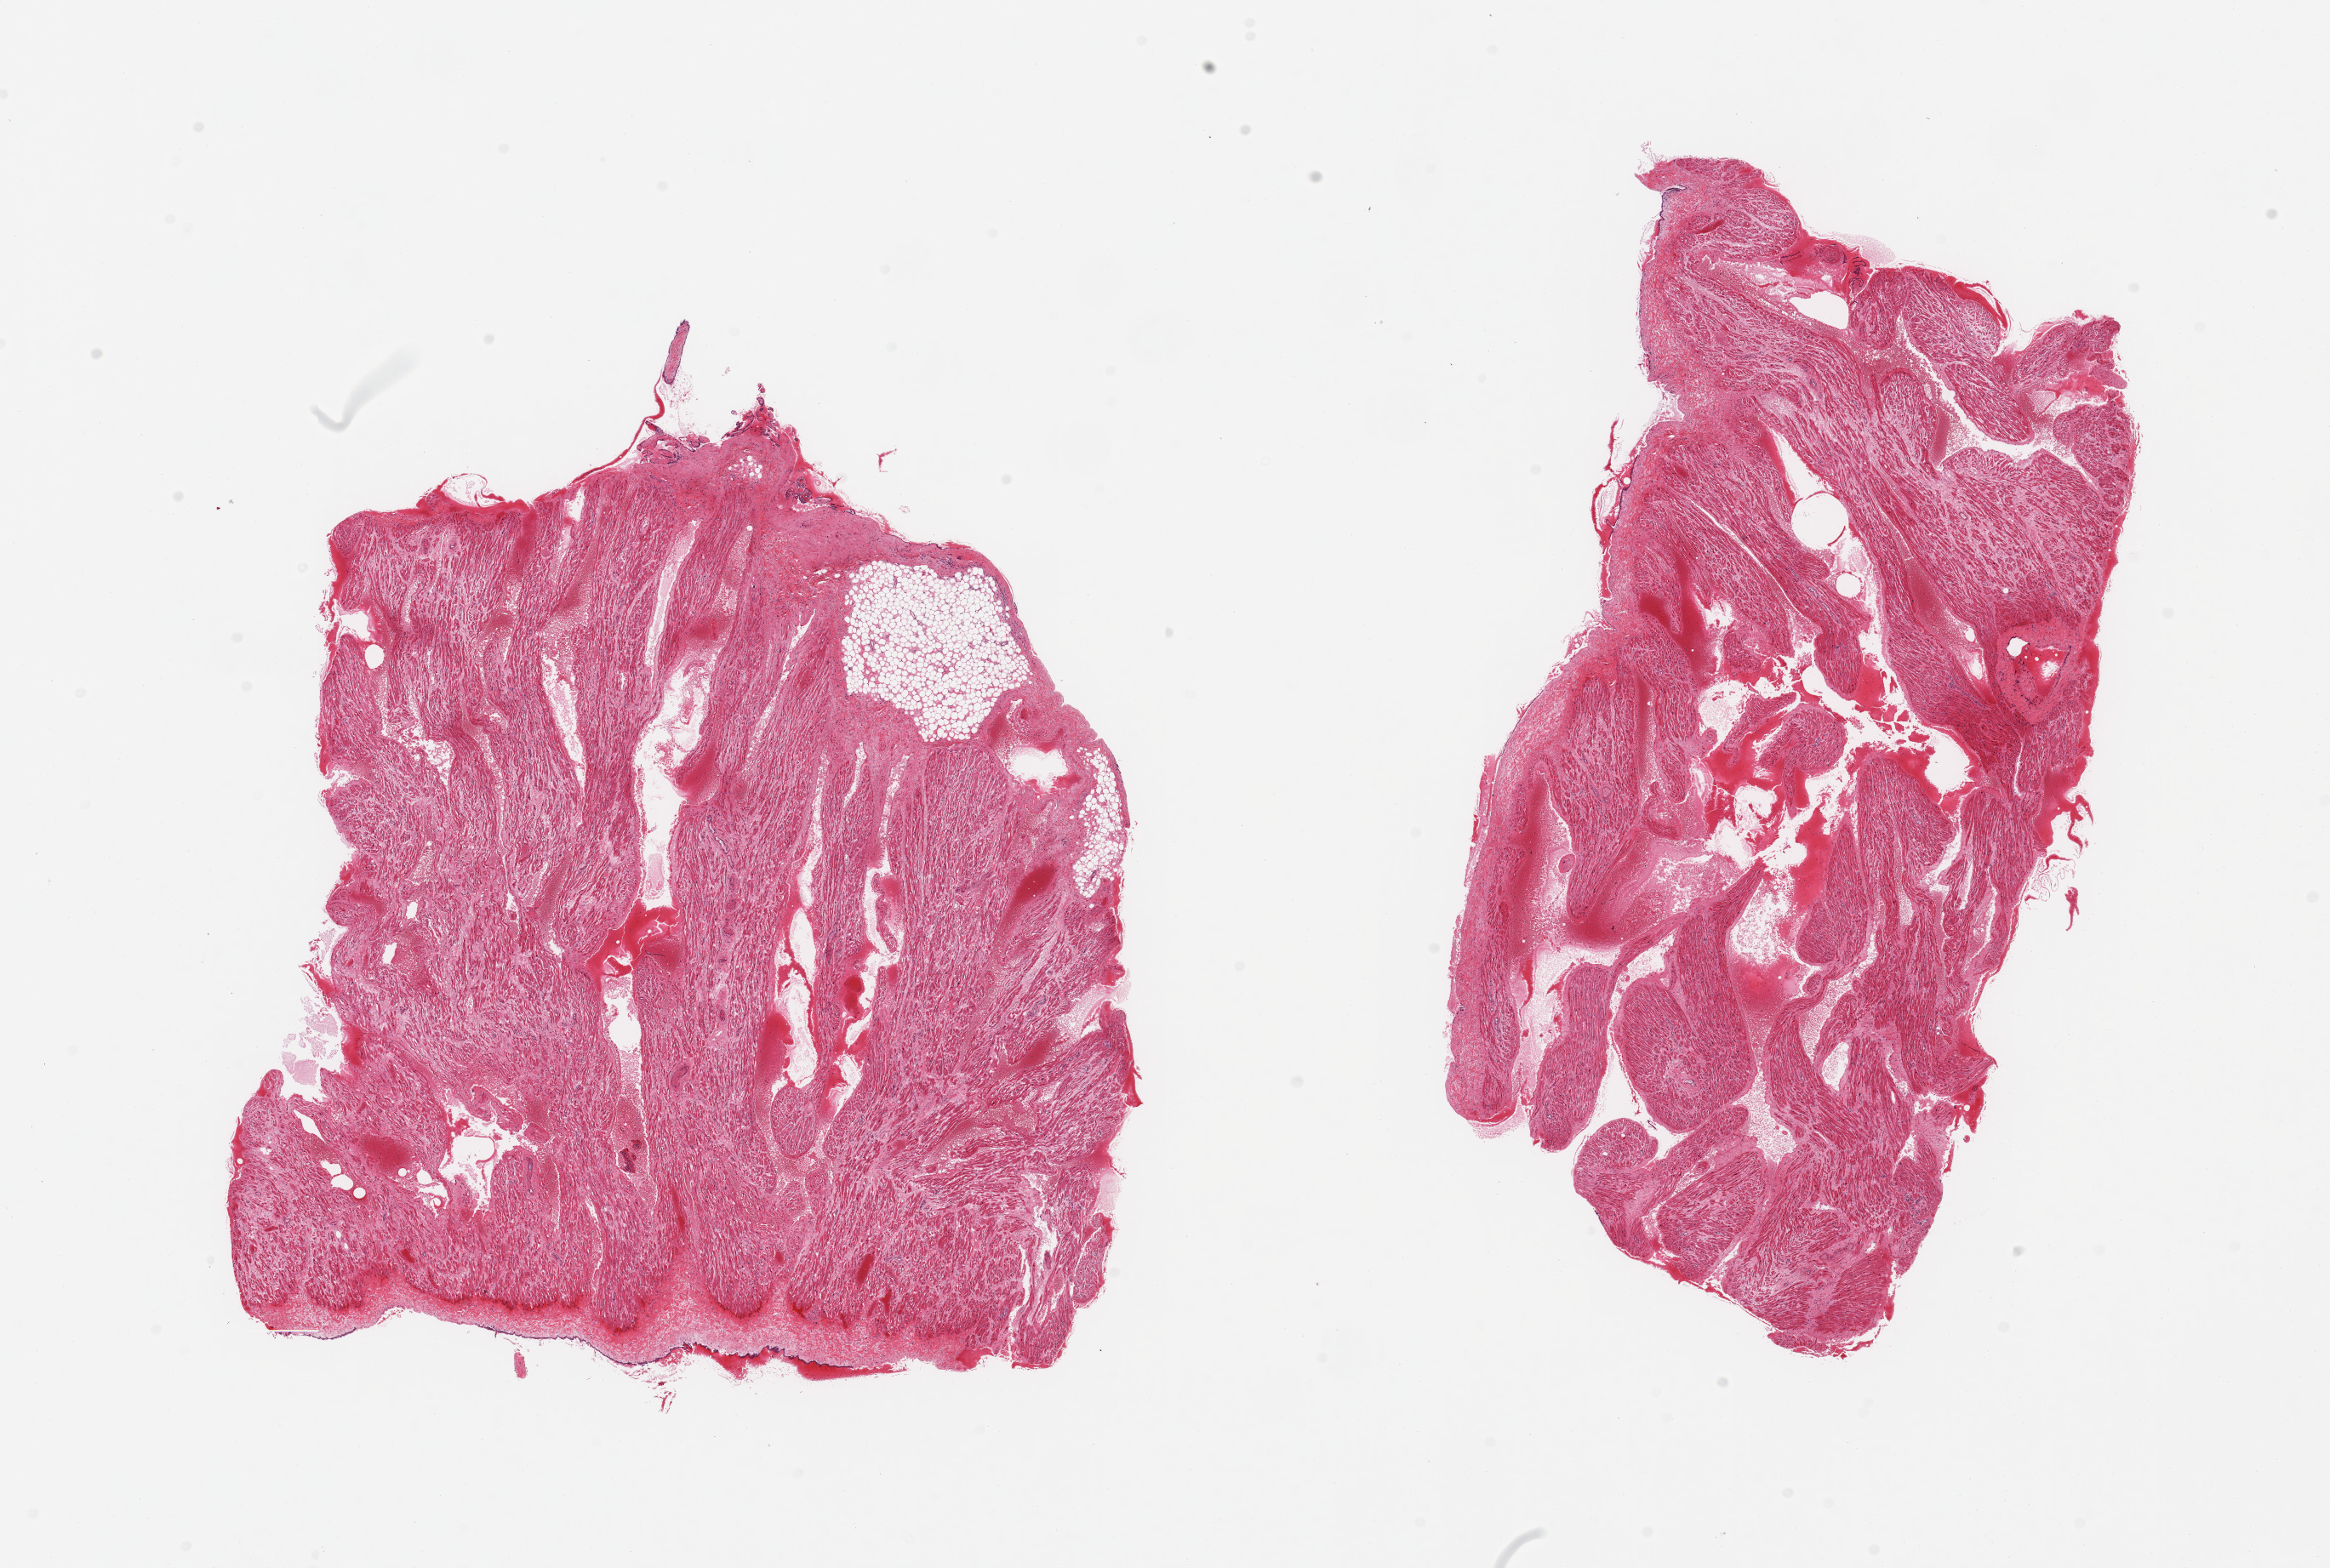
Whole-slide image, haematoxylin and eosin stain — low-resolution overview of the scanned area, about 21.7 x 14.6 mm. PAXgene-fixed, paraffin-embedded tissue. Section of auricular appendage (target tissue). Tissue donor sample.
Pathologist's review note for this sample: 2 pieces, no abnormalities.